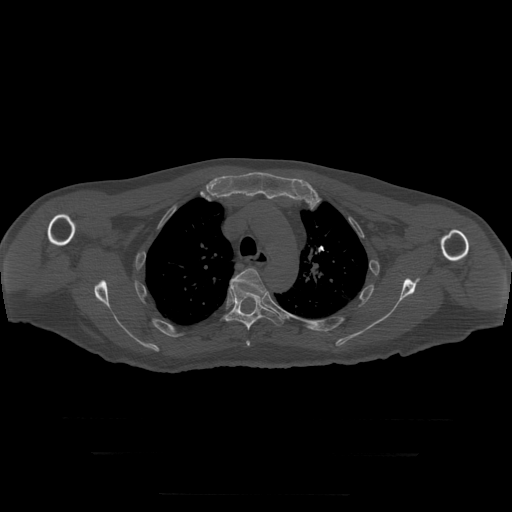
CT including the spine, one axial slice. Position 230 of 397 along the scan axis. Reconstruction kernel STANDARD. 120 kVp. Bone window (W 1800 / L 400 HU). 1.25 mm slice thickness. 512 × 512 image matrix, field of view 510 × 510 mm. Patient age 73 years. From the clinical record (not read from this slice): primary cancer: prostate.
Annotated regions visible in this slice (semi-automatically segmented with operator editing):
- T4 vertebra: bounding box [x1, y1, x2, y2] px = [230, 269, 266, 346]
- T5 vertebra: [225, 282, 285, 331]